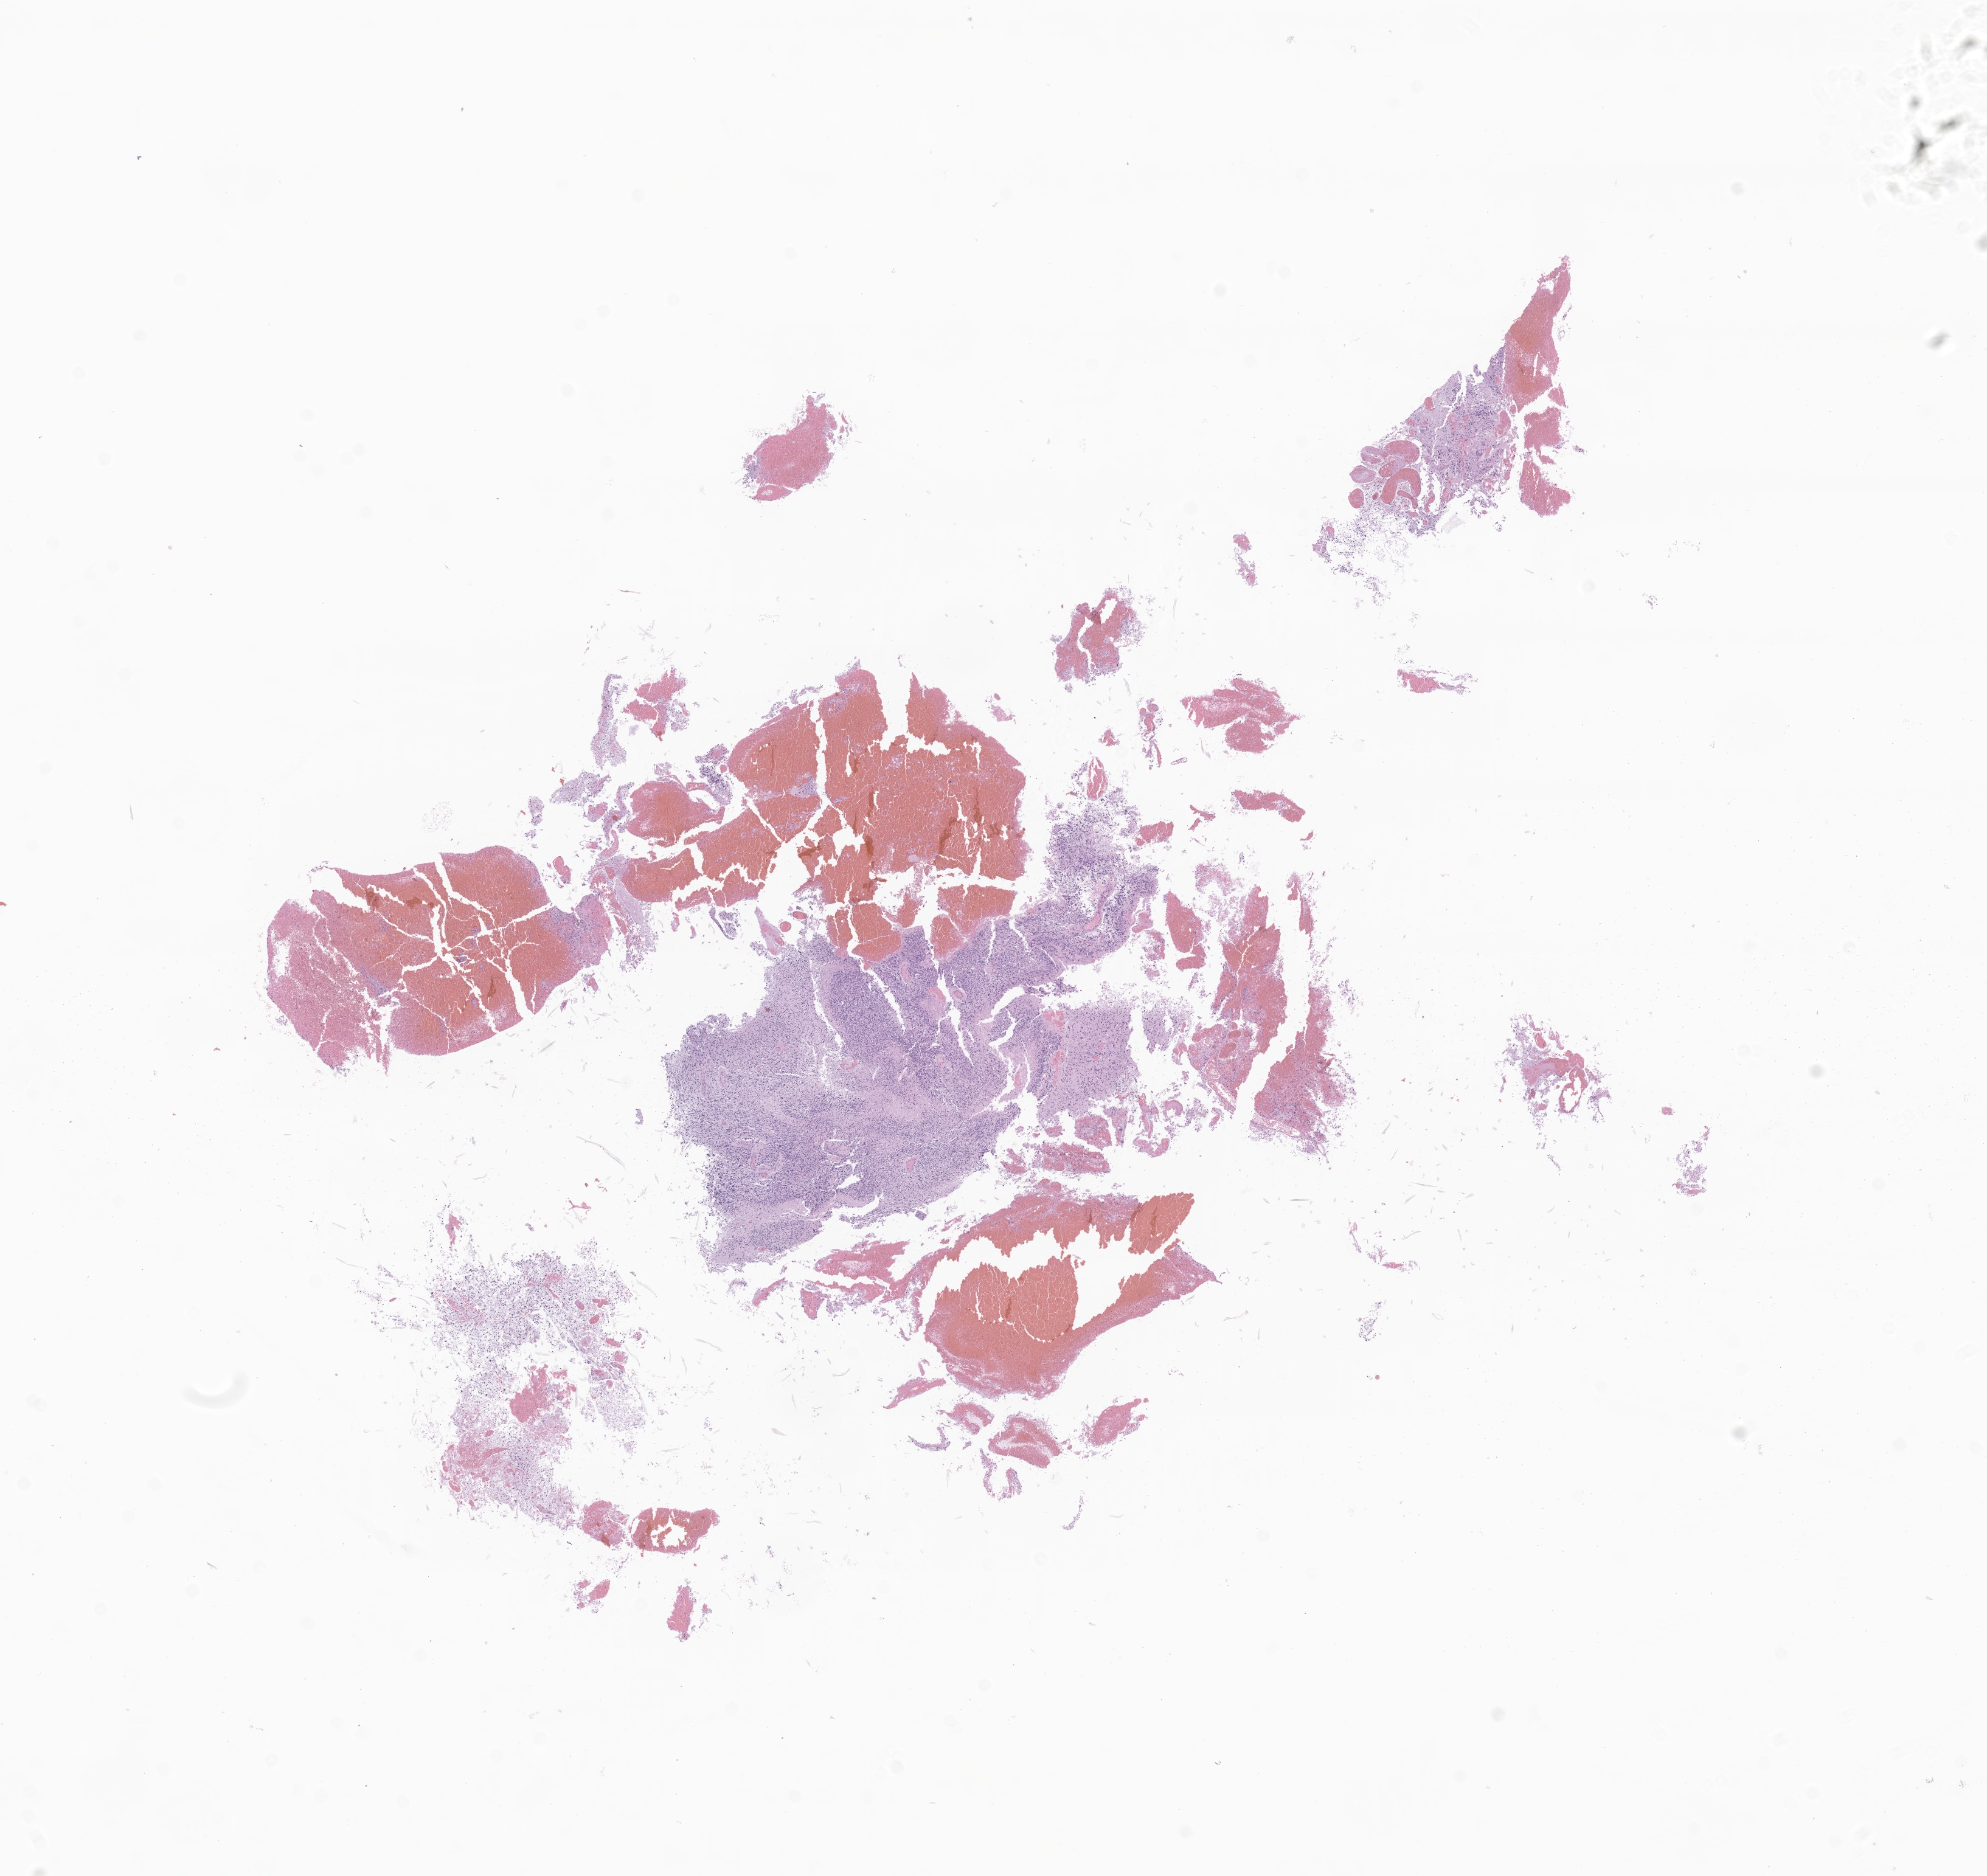
Digitized H&E-stained section of tumor tissue from the brain, whole scanned area (about 13.8 x 13.0 mm) shown as a low-resolution overview. Formalin-fixed, paraffin-embedded (FFPE) tissue. Patient: female, age 111 months (9 years 3 months).
Diagnosis (ICD-O-3 morphology term): Glioma, malignant.